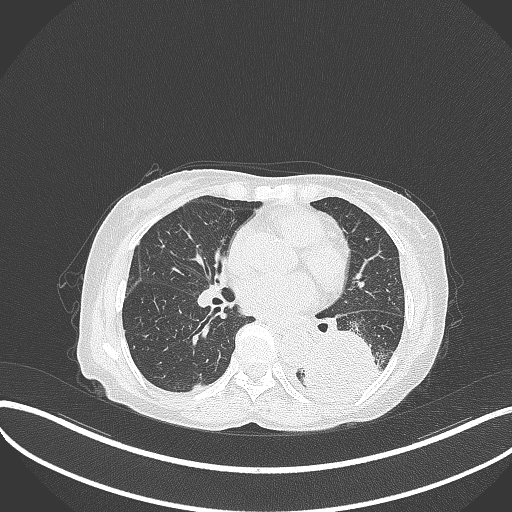
Chest CT, one axial slice. Slice 144 of 370 in the series (ordered by position). Reconstruction kernel B70f. 120 kVp. Lung window (W 1500 / L -600 HU). 1 mm slice thickness. 512 × 512 image matrix, field of view 400 × 400 mm. Patient: female, 78 years. Case-level facts recorded for this patient, not image findings: clinical TNM (as recorded): T3 N0 M1.
Annotated regions visible in this slice (bounding box drawn by a radiologist):
- lung tumour (recorded histology: squamous cell carcinoma): box from (x=302, y=328) to (x=382, y=406) px